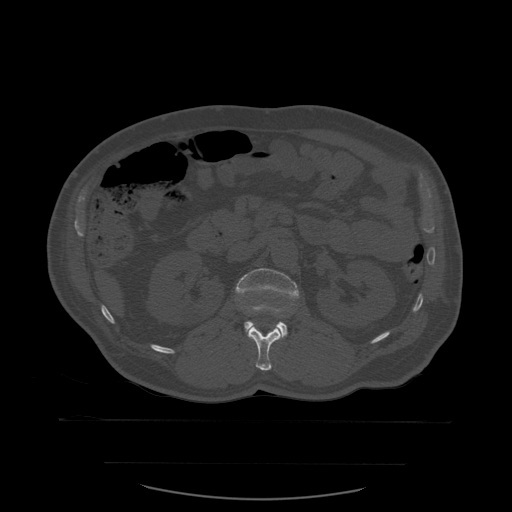
CT including the spine, one axial slice; slice 234 of 590 in the series (ordered by position); bone window (W 1800 / L 400 HU); 1.25 mm slice thickness; 512 × 512 image matrix, field of view 479 × 479 mm. Patient age 71 years. Case-level facts recorded for this patient, not image findings: primary cancer: lung.
Structures marked on this image (semi-automatic segmentation, software-assisted and operator-edited):
- L1 vertebra: bounding box (x1, y1, x2, y2) in pixels: (248, 326, 282, 371)
- L2 vertebra: (236, 269, 300, 340)